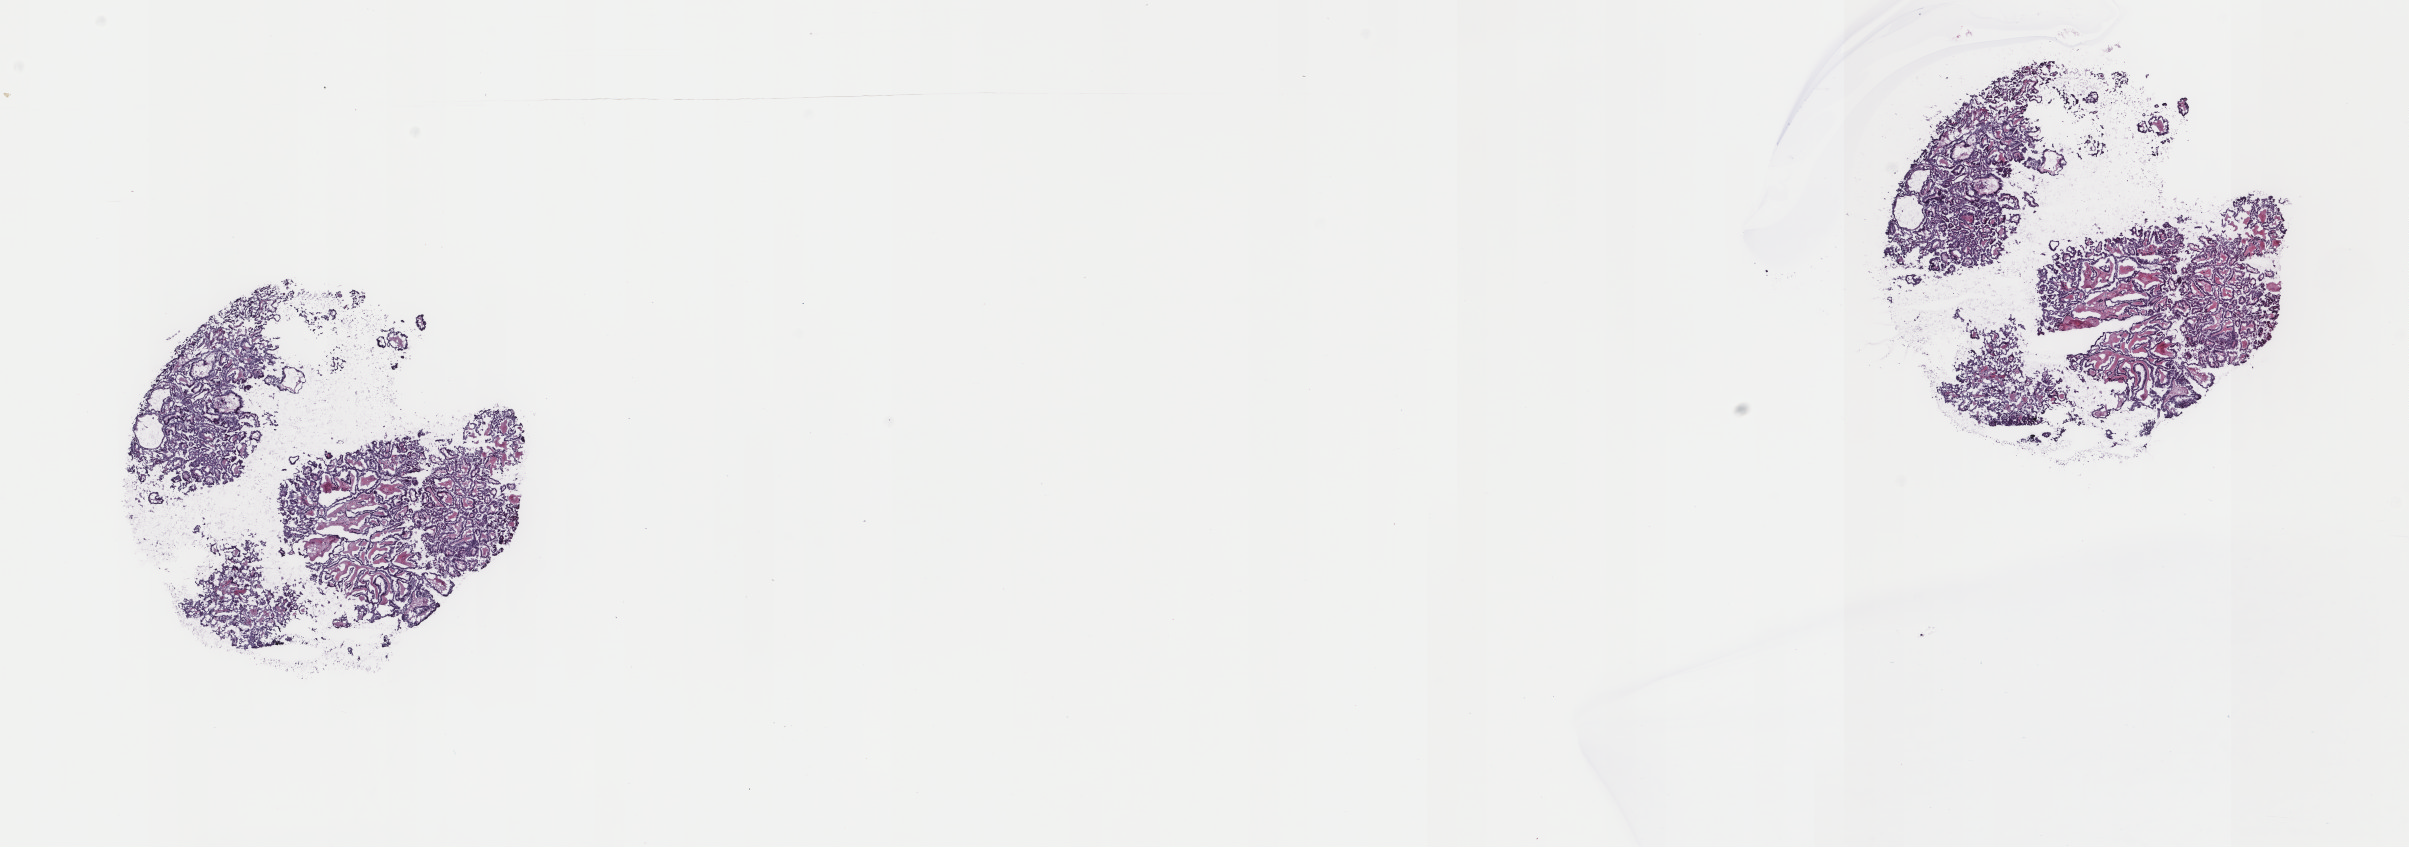
Hematoxylin and eosin (H&E) stained whole-slide image, a low-resolution overview of the entire scanned area, about 19.1 x 6.7 mm (acquisition: 40x scan). Frozen section. Sample: primary tumour, thyroid. Patient: male, age at initial diagnosis 40 years. Pathologist review of this section (percent, as recorded): tumour cells 80%, tumour nuclei 80%, normal cells 0%, stromal cells 20%, necrosis 0%. Infiltration values recorded for this section: lymphocyte infiltration 1%, monocyte infiltration 1%, neutrophil infiltration 0%.
Lymph nodes positive (case pathology): 0 of 3 examined. Diagnosis: Papillary adenocarcinoma, NOS (thyroid gland). Laterality: midline. TNM: T3 N0 MX. AJCC pathologic stage: I.